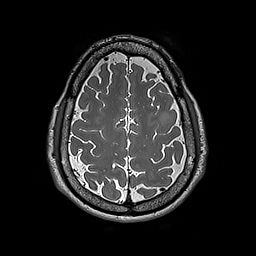
Brain MRI from a brain-tumour surgery series, one axial slice. Position 64 of 192 along the scan axis. 1 mm slice thickness. 256 × 256 image matrix, field of view 250 × 250 mm. From the clinical record (not read from this slice): histopathology: Astrocytoma; WHO grade: 2; IDH mutation: yes.
Annotated regions visible in this slice (expert manual segmentation):
- tumour: box from (x=159, y=111) to (x=173, y=124) px